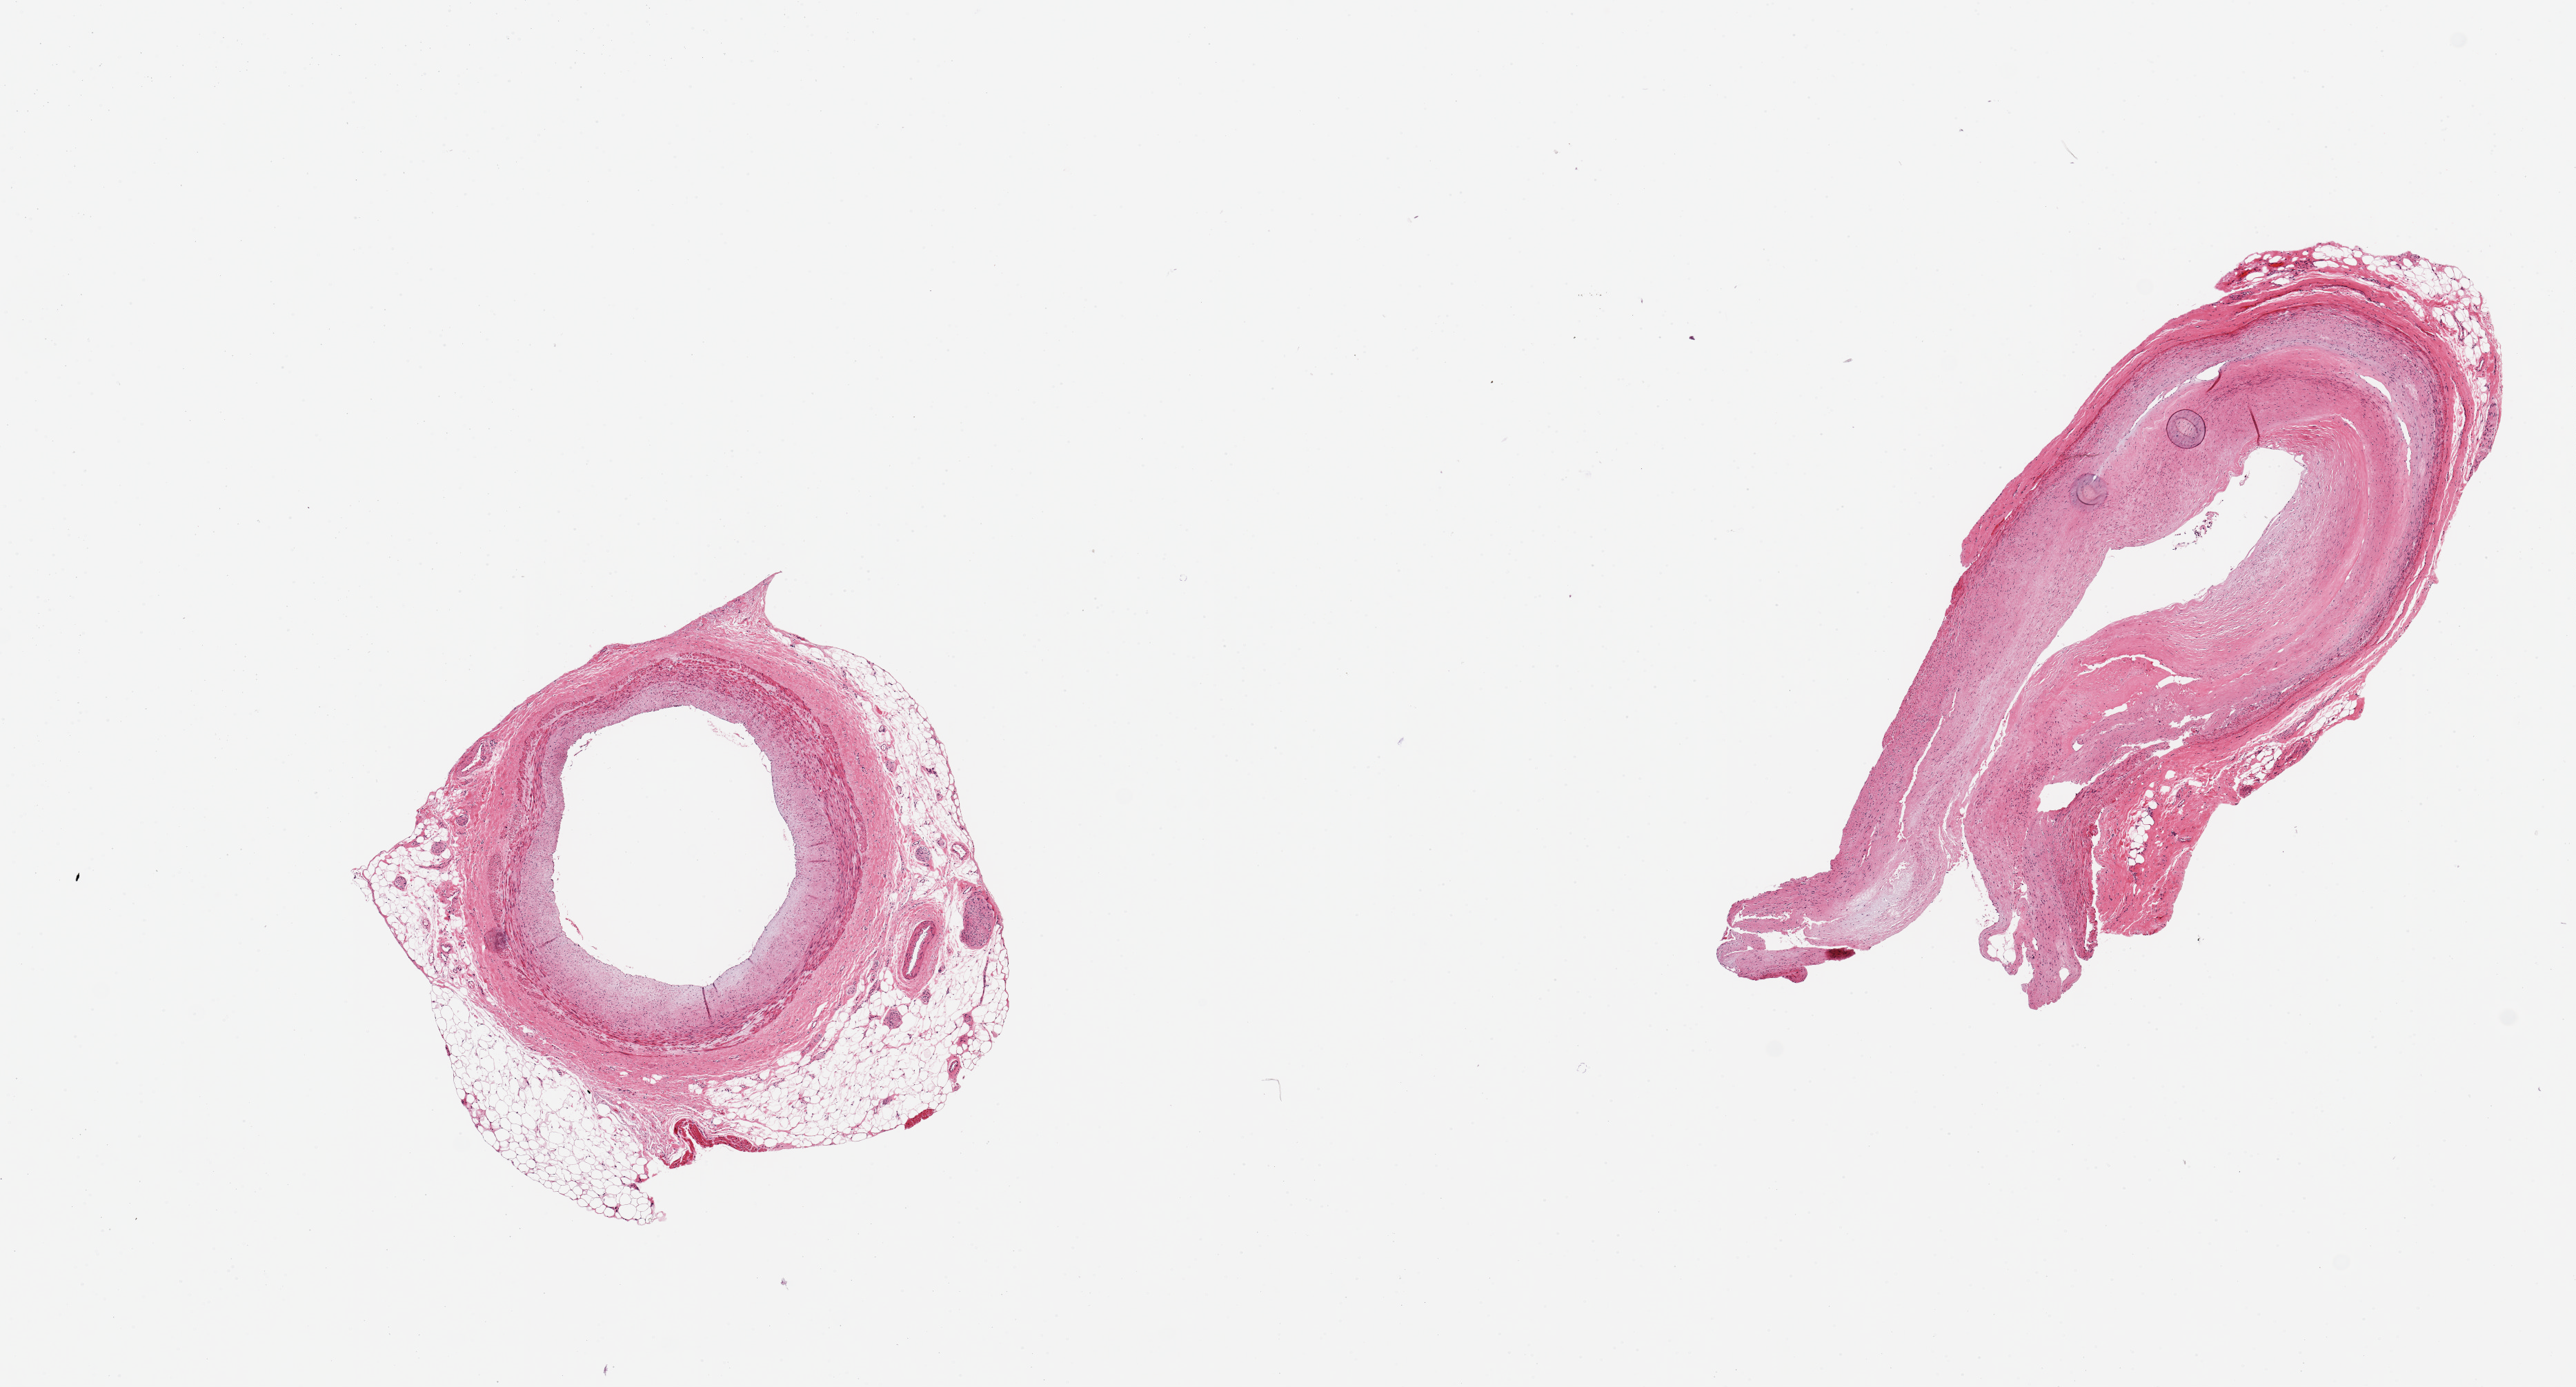
Digitized H&E-stained section — whole scanned area (about 14.8 x 8.0 mm, acquisition: 20x scan) shown as a low-resolution overview; PAXgene-fixed, paraffin-embedded tissue; section of coronary artery (target tissue); tissue donor sample. Donor: male.
Reviewer comment on this tissue sample: 2 pieces, ~2.7mm diameter ; ~20% adipose tissue around one and 5% around the other; eccentric intimal fibrosis.